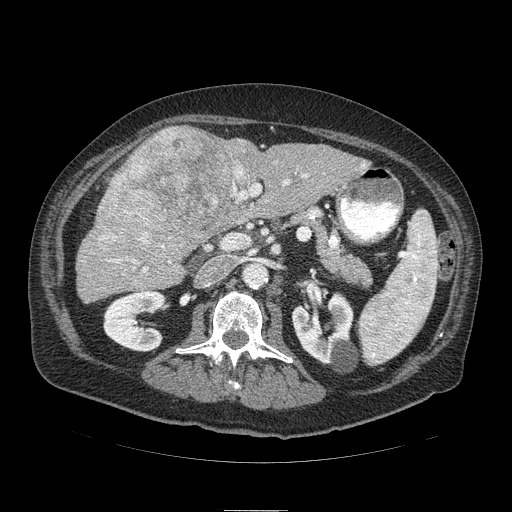
Contrast-enhanced abdominal CT (liver protocol), one axial slice. Position 41 of 103 along the scan axis. 120 kVp. Soft-tissue window (W 400 / L 40 HU). 2.5 mm slice thickness. 512 × 512 image matrix. Case-level facts recorded for this patient, not image findings: diagnosis: hepatocellular carcinoma (patient treated with transarterial chemoembolisation; whether this scan precedes or follows treatment is not stated here); TNM stage (as recorded): Stage-IIIA; Child-Pugh class: B; tumour differentiation: well differentiated; tumour nodularity: multinodular.
Annotated regions visible in this slice (semi-automatic segmentation, software-assisted and operator-edited):
- liver parenchyma outside the tumour (the mass and vessels are separate outlines, so this box may not span the whole liver): bounding box (x1, y1, x2, y2) in pixels: (76, 138, 370, 302)
- mass: (90, 125, 258, 263)
- liver vessels: (108, 165, 365, 273)